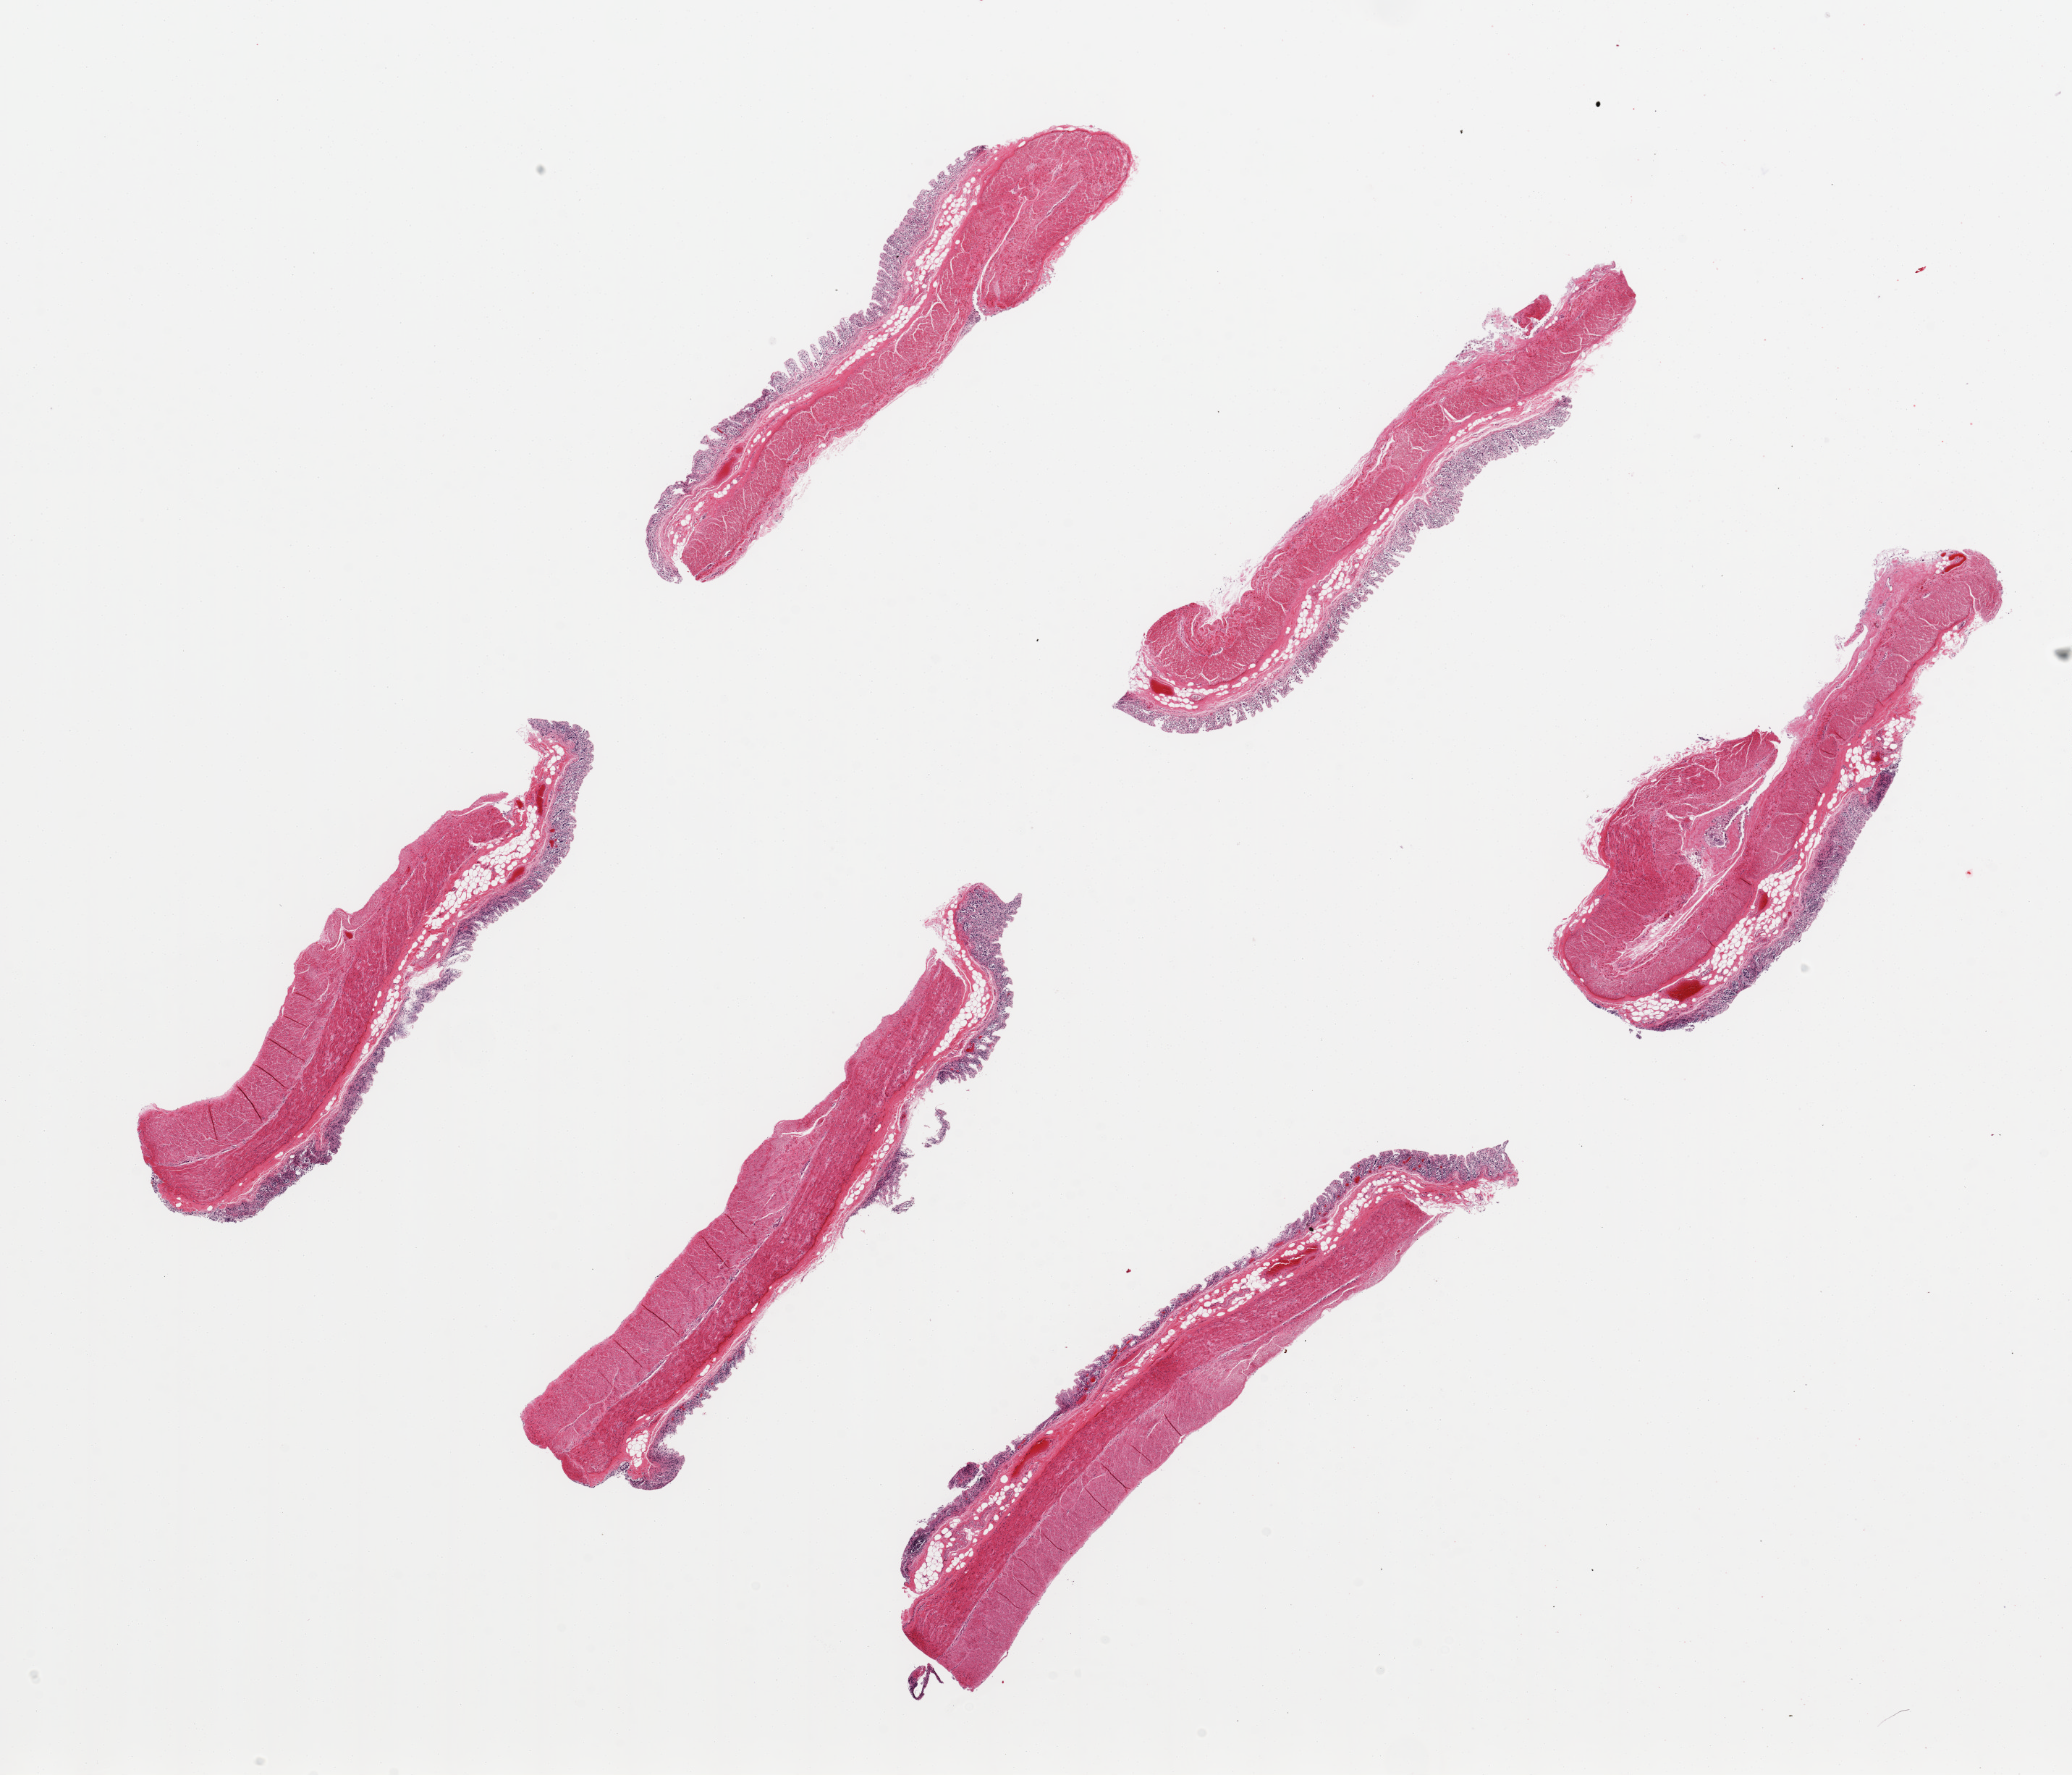
Hematoxylin and eosin (H&E) whole-slide image — shown as a low-resolution overview of the whole scanned area (about 22.6 x 19.4 mm, acquisition: 20x scan), PAXgene-fixed, paraffin-embedded tissue, section of transverse colon (target tissue), tissue donor sample. Donor sex: male.
Reviewer comment on this tissue sample: 6 pieces up to 8x2.5 mm; mucosa completely autolyzed; muscle slightly autolyzed.